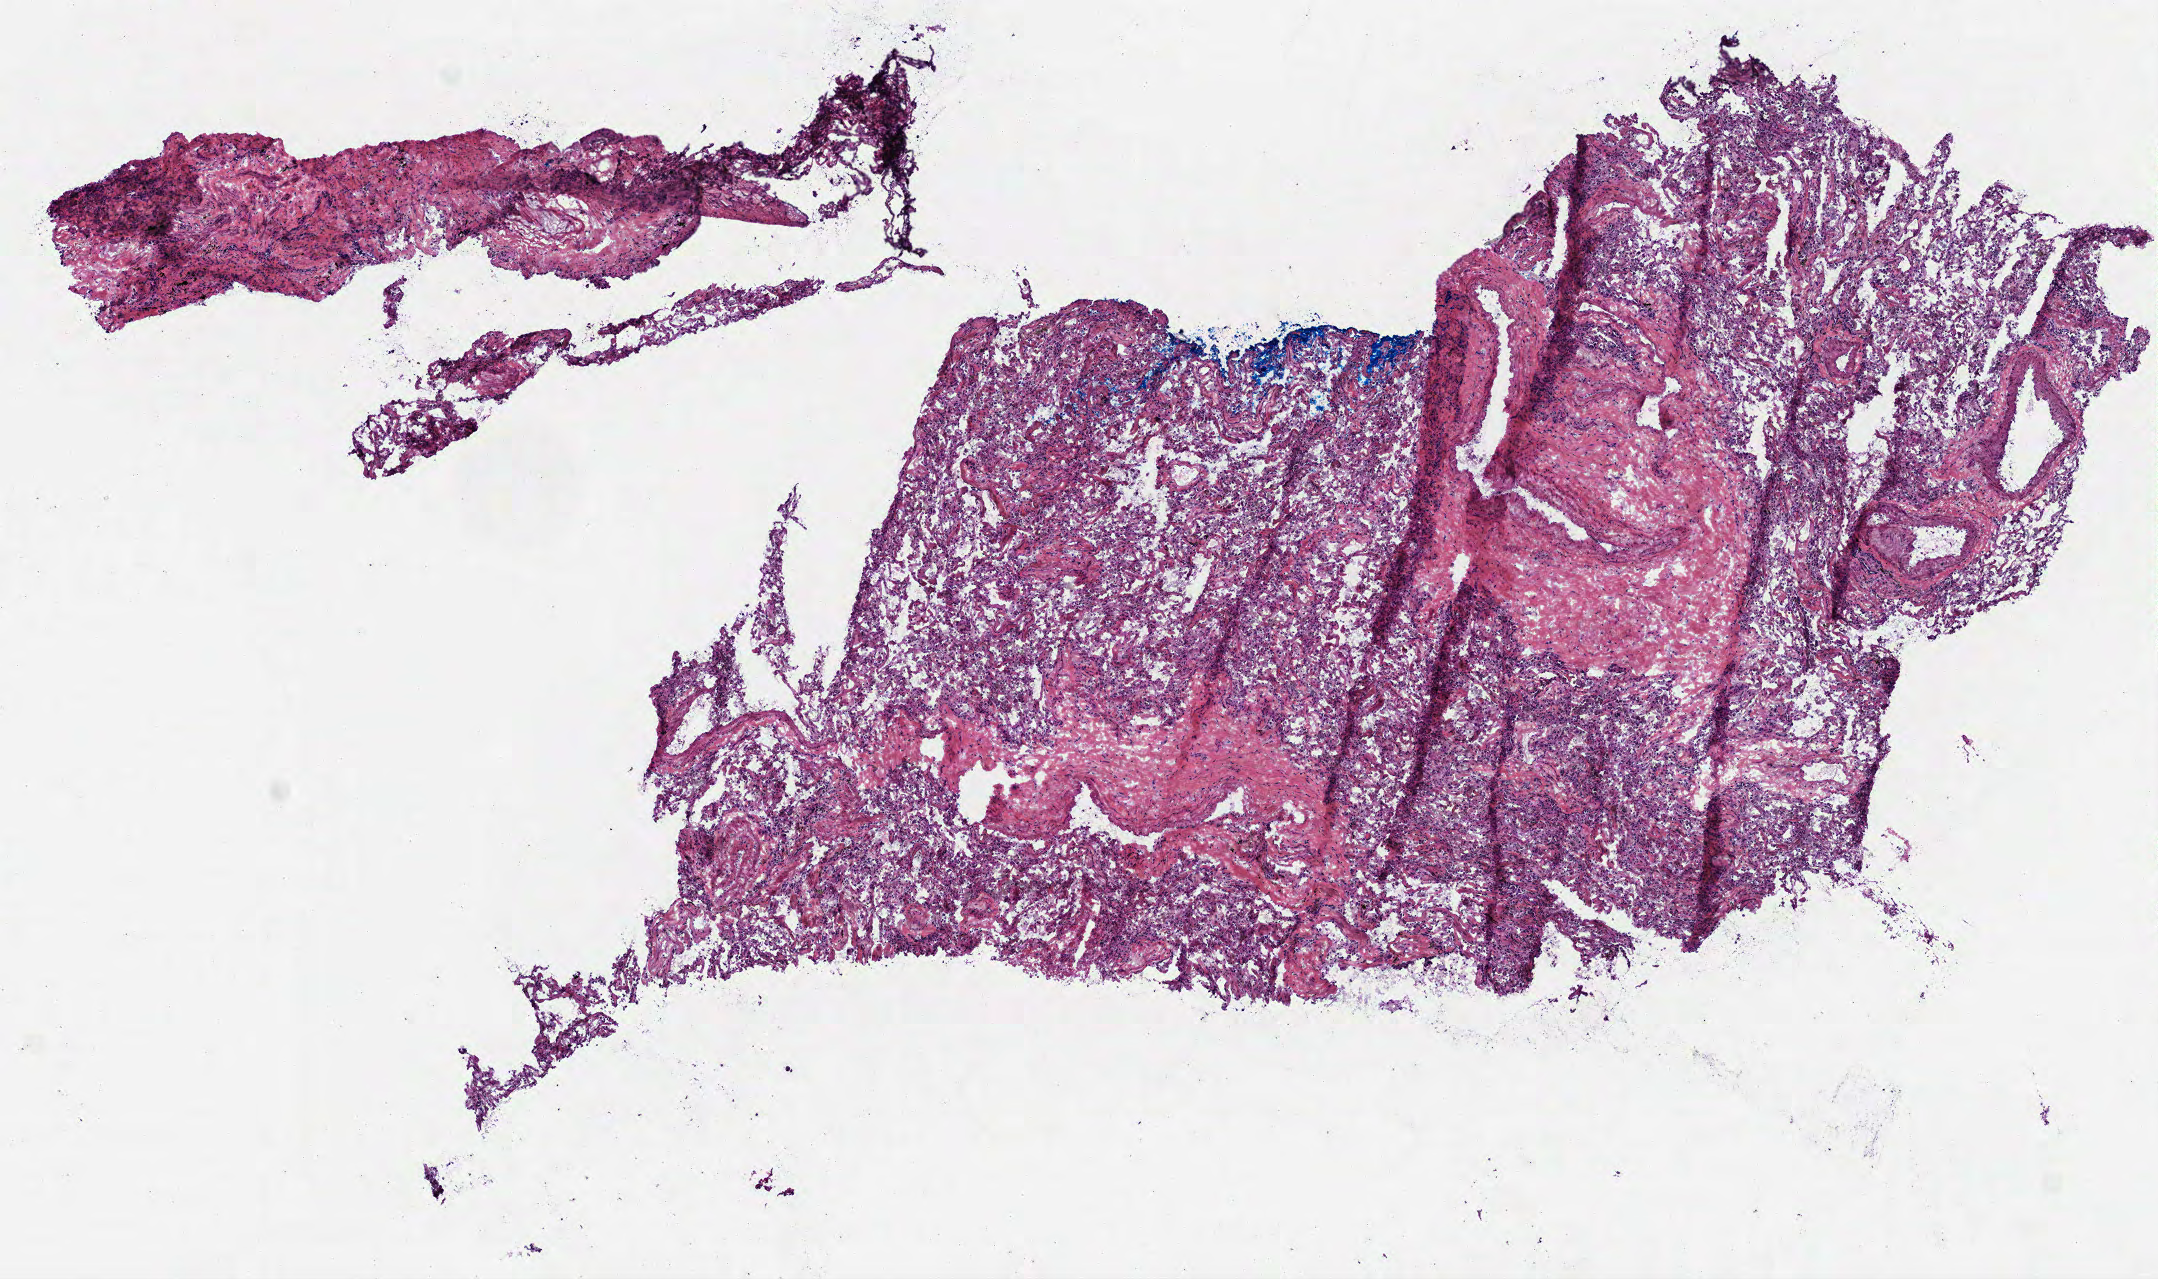
Whole-slide histology image, Hematoxylin and eosin (H&E) stained — shown as a low-resolution overview of the whole scanned area (about 8.7 x 5.2 mm, acquisition: 40x scan). Frozen section from the top of the tissue portion. Solid tissue normal (non-tumour tissue) sample from the lung. Female, age 55 years at initial diagnosis.
This section: solid tissue normal (non-tumour) sample from the same patient. Patient diagnosis: Squamous cell carcinoma, NOS (lower lobe, lung).